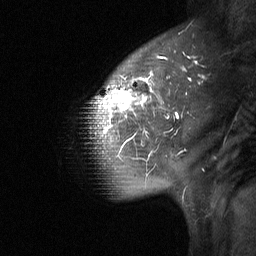
Breast MRI (dynamic contrast-enhanced), one sagittal slice. Position 48 of 64 along the scan axis. Dynamic contrast-enhanced study with each time point stored as its own series, time point 2 of 3 at this slice position (early post-contrast, ordered by acquisition time). 1.5 T. TE 4.8 ms, TR 27 ms. 2 mm slice thickness. 256 × 256 image matrix, field of view 200 × 200 mm. Female patient, age 42 years. Case-level facts recorded for this patient, not image findings: setting: breast cancer imaged before/during neoadjuvant chemotherapy; receptor status: triple-negative.
Outlined on this slice (semi-automatic segmentation, software-assisted and operator-edited):
- analysis volume of interest (the breast-tissue region the enhancement analysis was run in; not a lesion): bounding box <89,33,203,190> (left, top, right, bottom; pixels)
- tumour enhancement mask (voxels above the 90 % enhancement threshold inside the analysis volume of interest): <96,56,196,137>